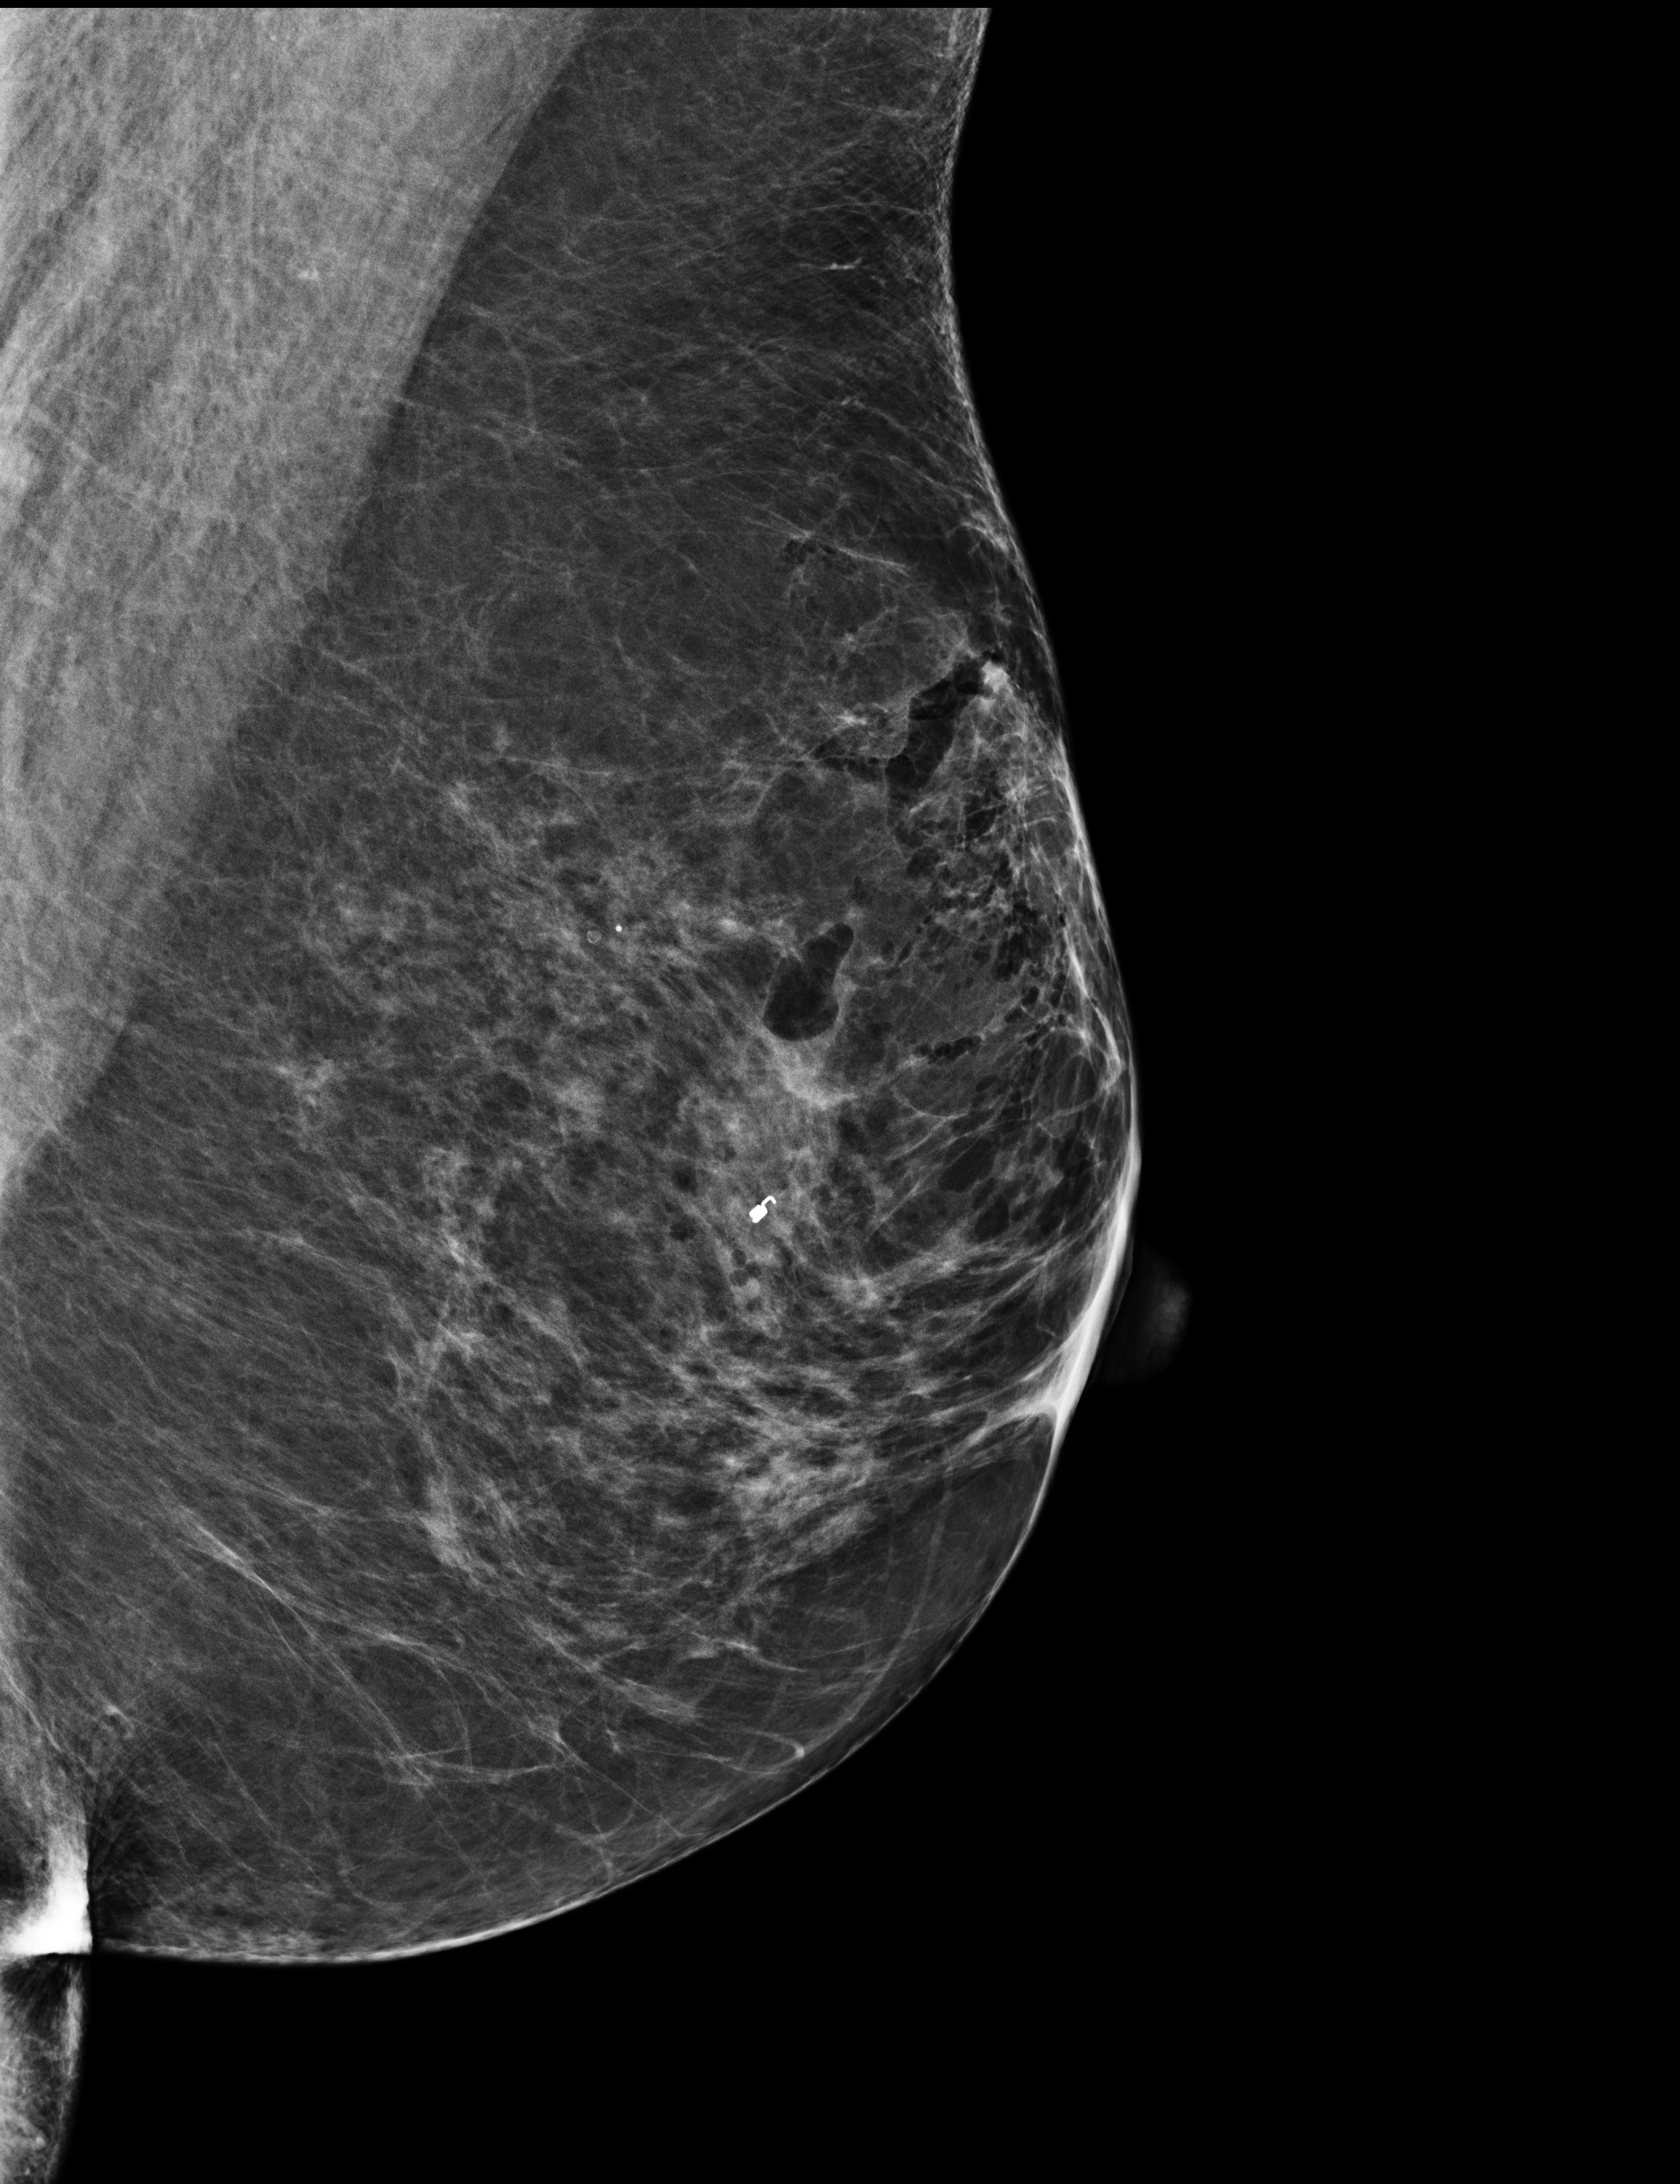
Diagnostic examination (additional views). Patient aged 74 years (female).
Image type: full-field digital mammogram. Breast: left. Projection: mediolateral oblique (MLO) view.